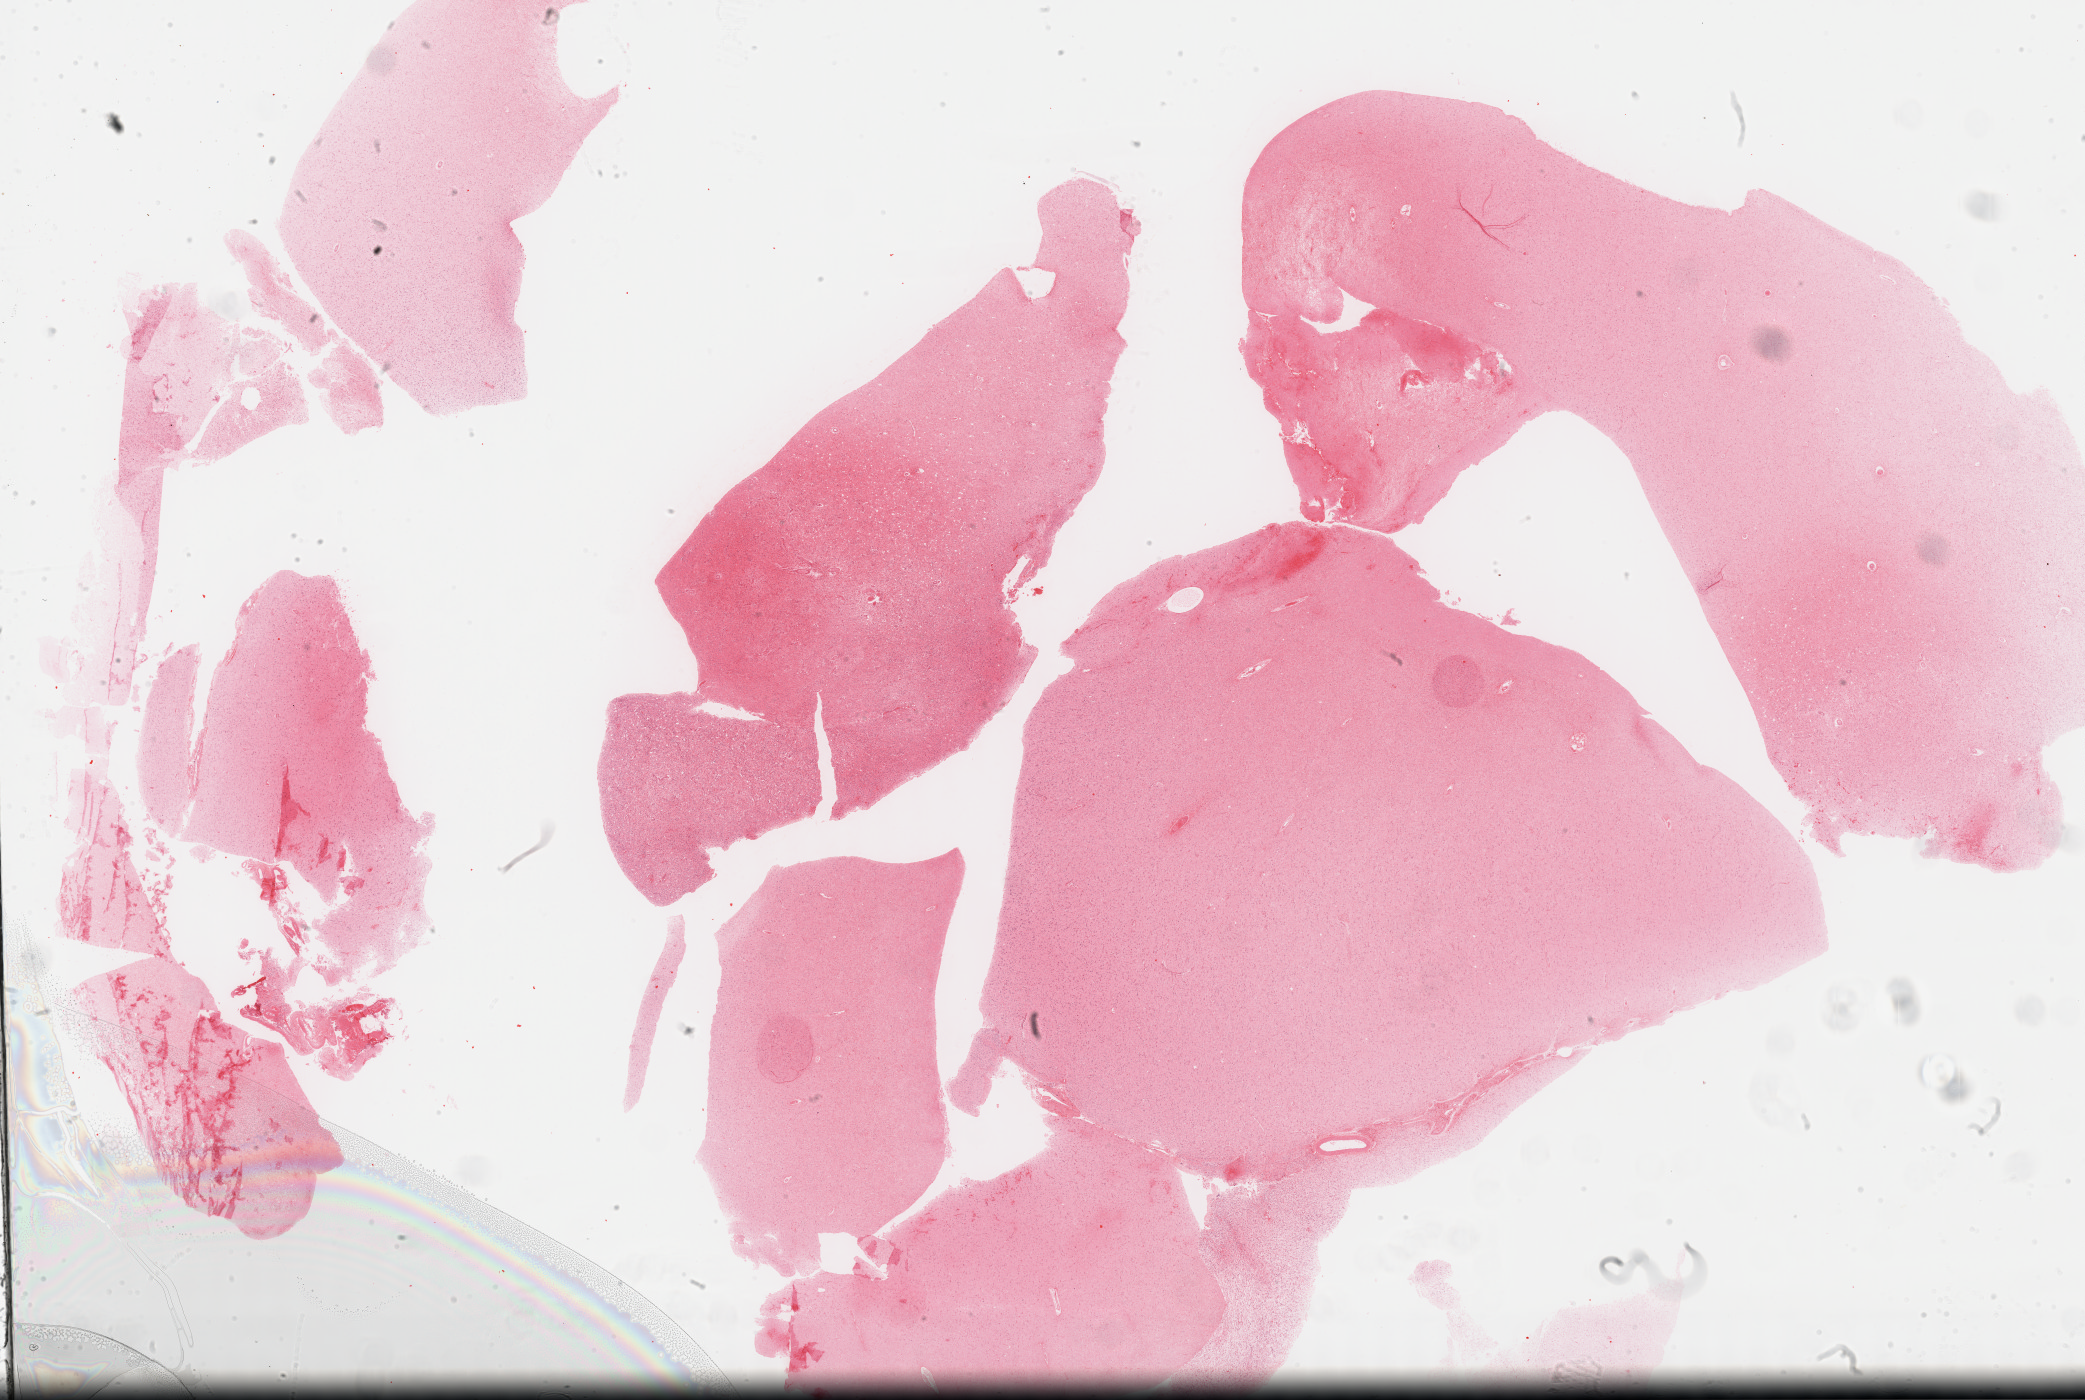
Digitized H&E-stained tissue section (whole slide) — low-resolution overview of the scanned area, about 33.7 x 22.6 mm (slide scanned at 40x). Formalin-fixed paraffin-embedded (FFPE) diagnostic section. Primary tumour sample from the brain. Patient: female, age at initial diagnosis 44 years. Histologic grade: G3 (poorly differentiated).
Diagnosis: Astrocytoma, anaplastic (cerebrum).